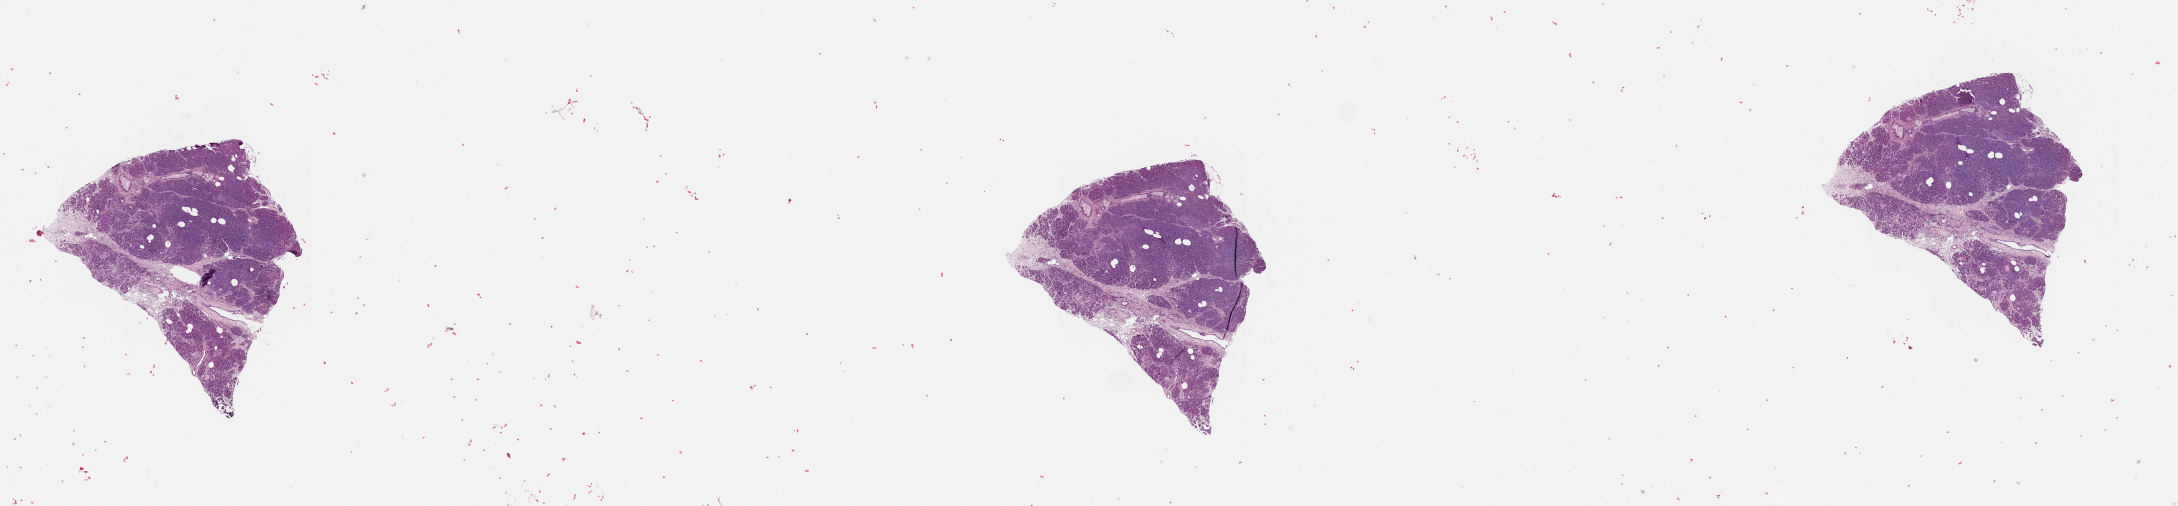
Digitized Hematoxylin and eosin (H&E) stained tissue section (whole slide) — whole scanned area (about 35.1 x 8.1 mm, slide scanned at 20x) shown as a low-resolution overview; normal (non-tumour) tissue sample, sampled site: pancreas. Female, 69 y/o.
This section: normal (non-tumour) tissue from the same patient. Patient diagnosis: Infiltrating duct carcinoma, NOS.